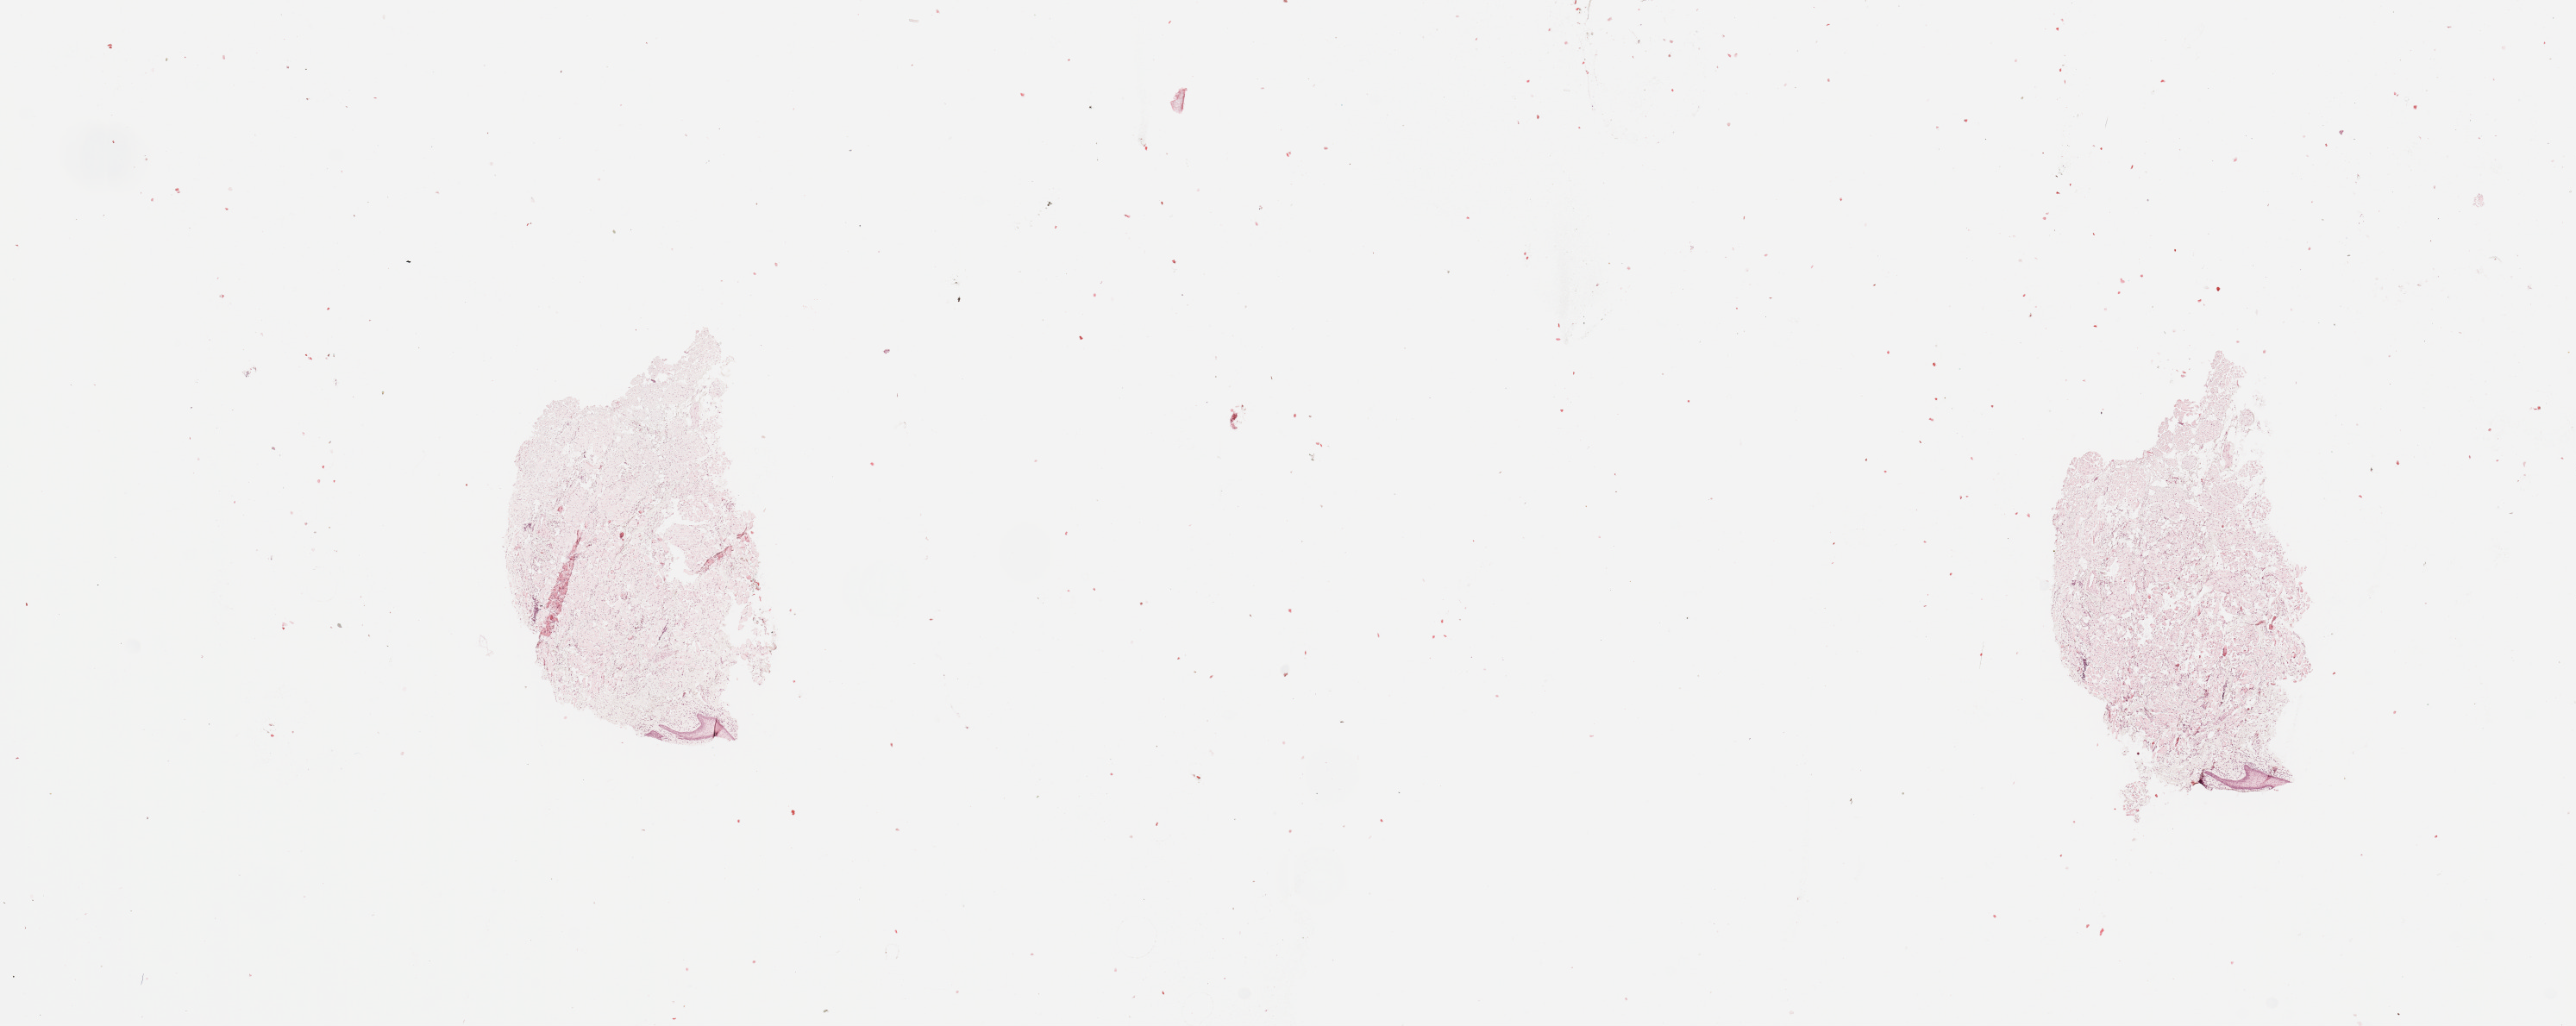
Whole-slide histology image, Hematoxylin and eosin (H&E) stained, a low-resolution overview of the entire scanned area, about 23.6 x 9.4 mm (acquisition: 20x scan), normal (non-tumour) tissue sample, sampled site: tongue. 55-year-old female patient.
* this section: normal (non-tumour) tissue from the same patient
* patient diagnosis: Squamous cell carcinoma, NOS (tongue, NOS)